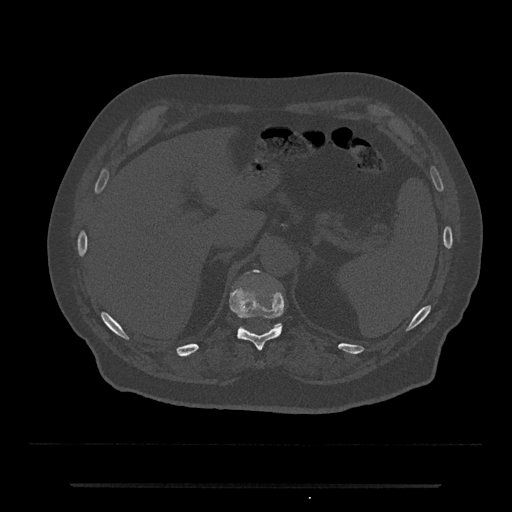
CT including the spine, one axial slice; slice 640 of 797 in the series (ordered by position); reconstruction kernel Br40s/3; 120 kVp; bone window (W 1800 / L 400 HU); 0.5 mm slice thickness; 512 × 512 image matrix, field of view 434 × 434 mm. Patient: male, 80 years. From the clinical record (not read from this slice): primary cancer: prostate.
Annotated regions visible in this slice (semi-automatic segmentation, software-assisted and operator-edited):
- T11 vertebra: bounding box (x1, y1, x2, y2) in pixels: (230, 289, 284, 351)
- T12 vertebra: (238, 269, 282, 331)